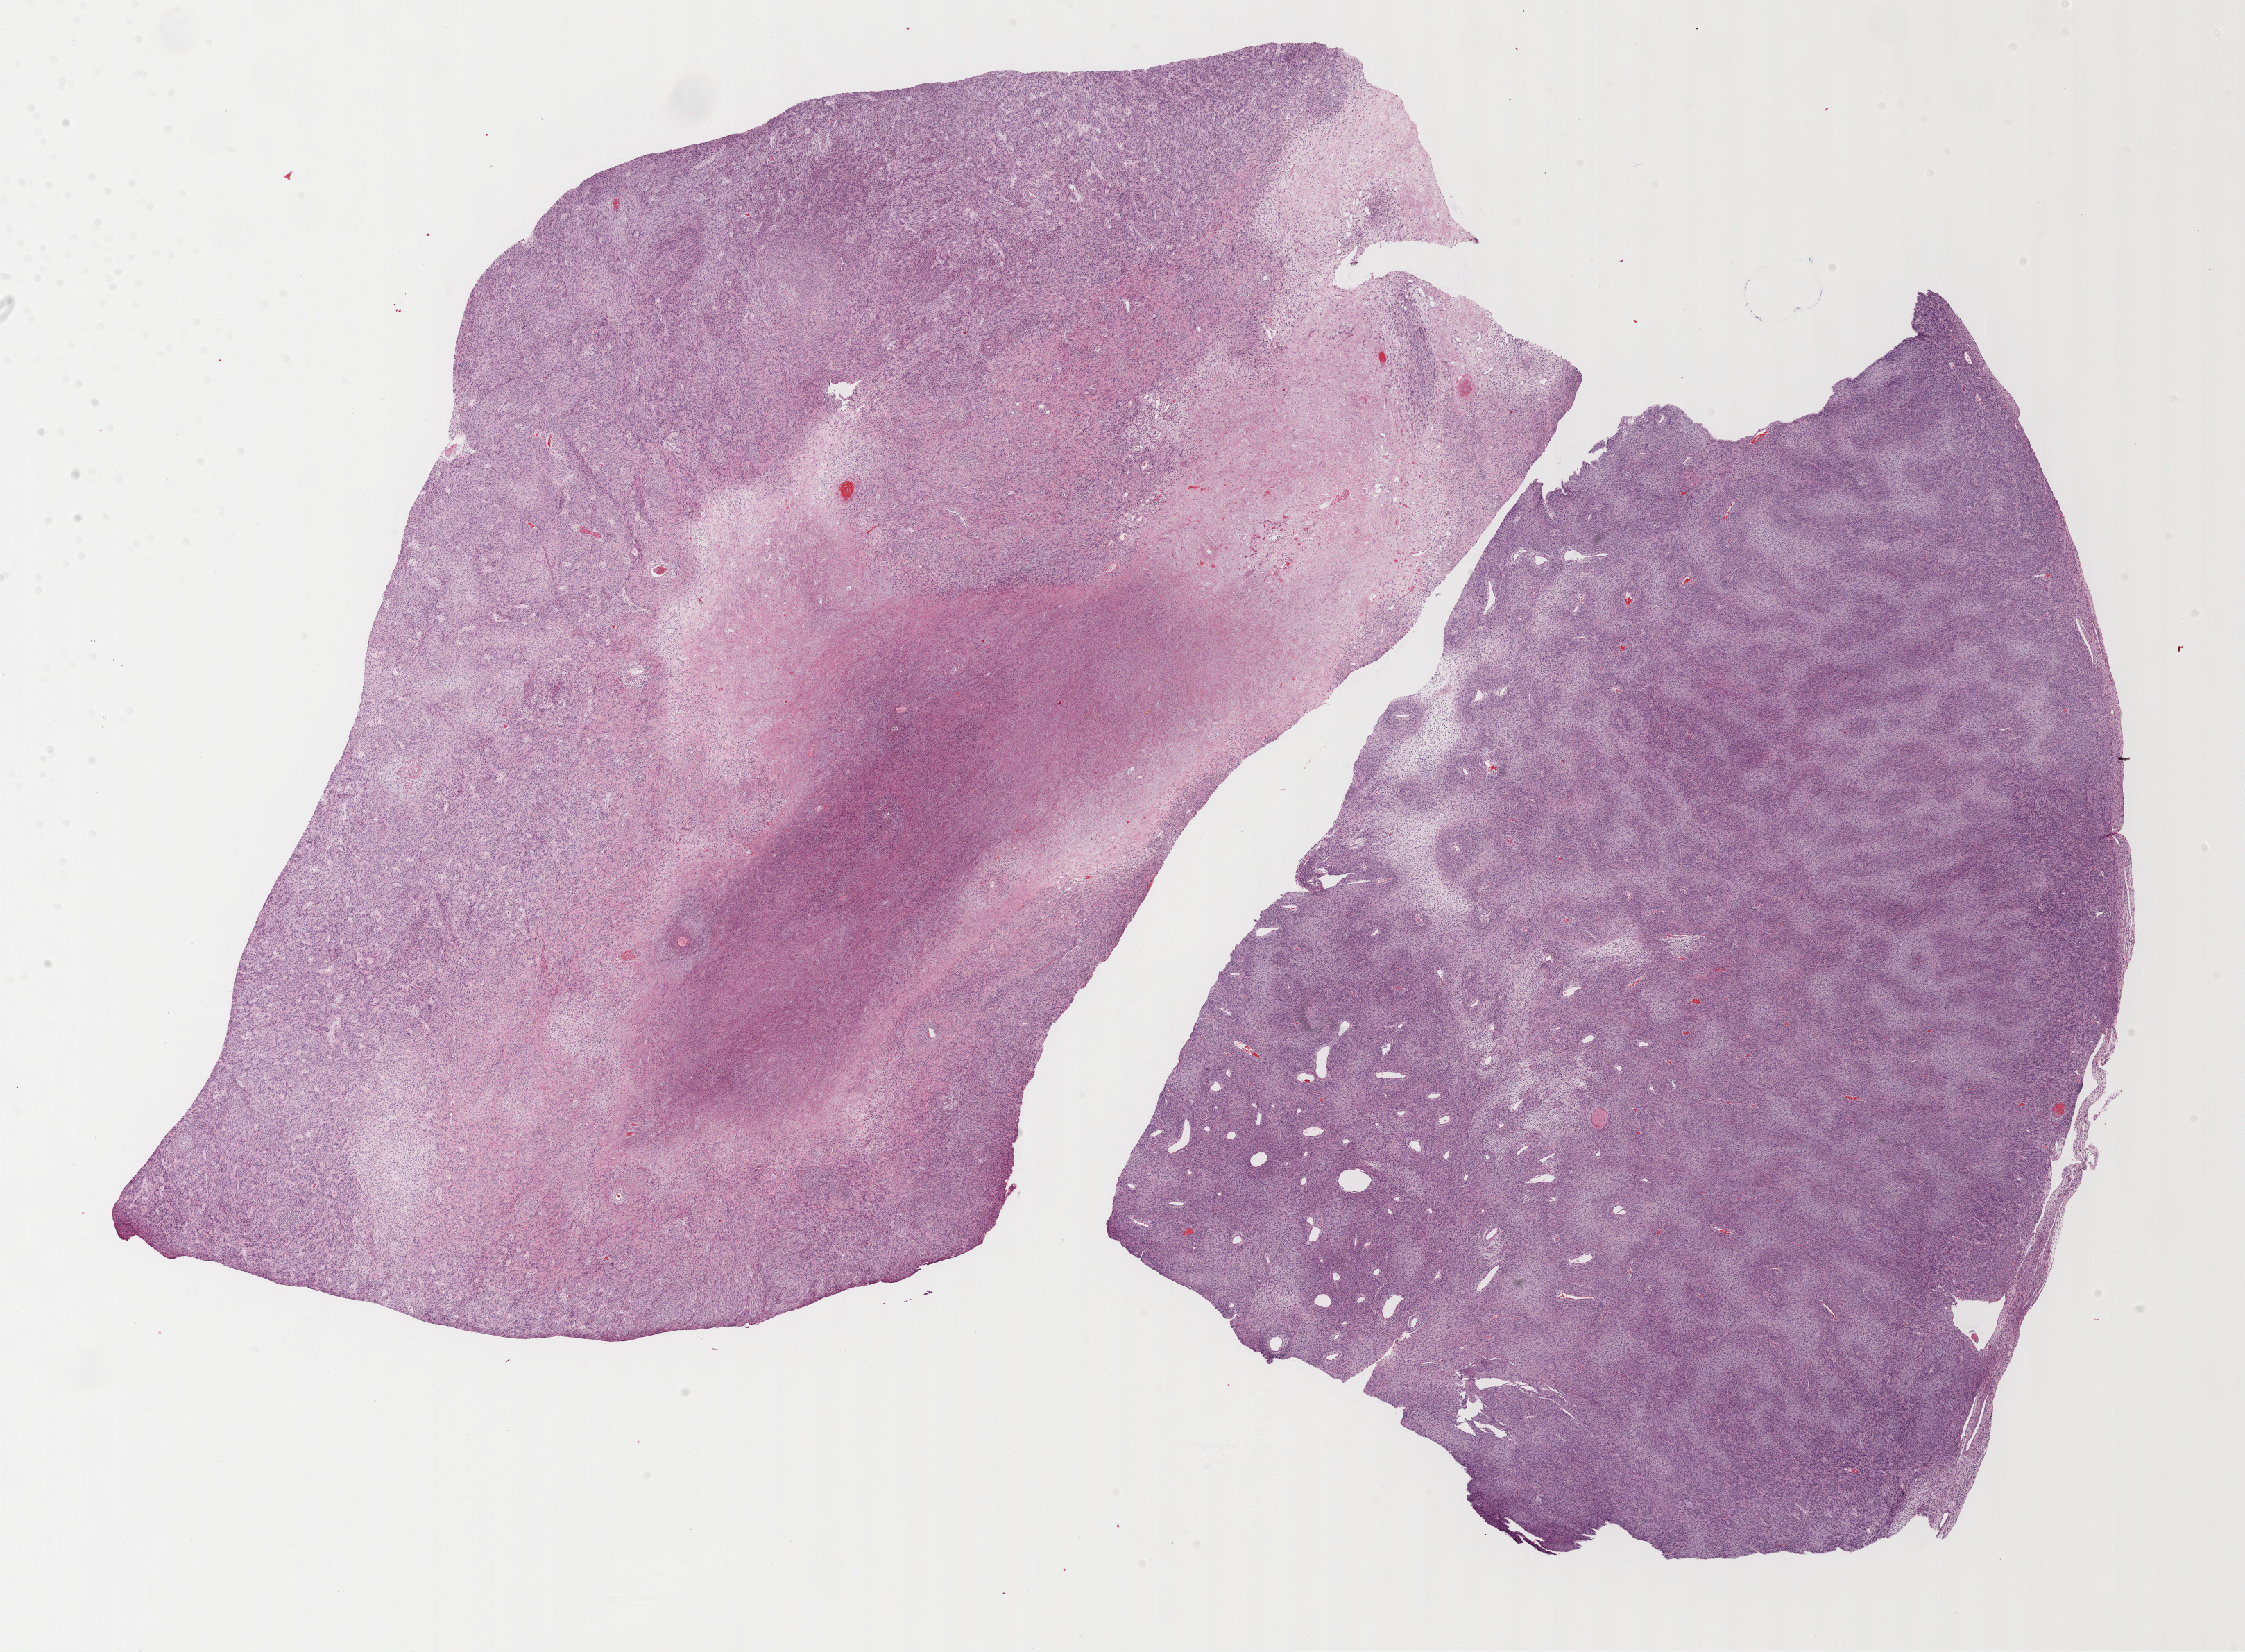
Whole-slide histology image, H&E — low-resolution overview of the scanned area, about 26.2 x 19.3 mm (acquisition: 40x scan); FFPE section; retroperitoneum and peritoneum, primary tumour sample. Male, age 52 years at initial diagnosis.
Pathologic diagnosis: Undifferentiated sarcoma (retroperitoneum).